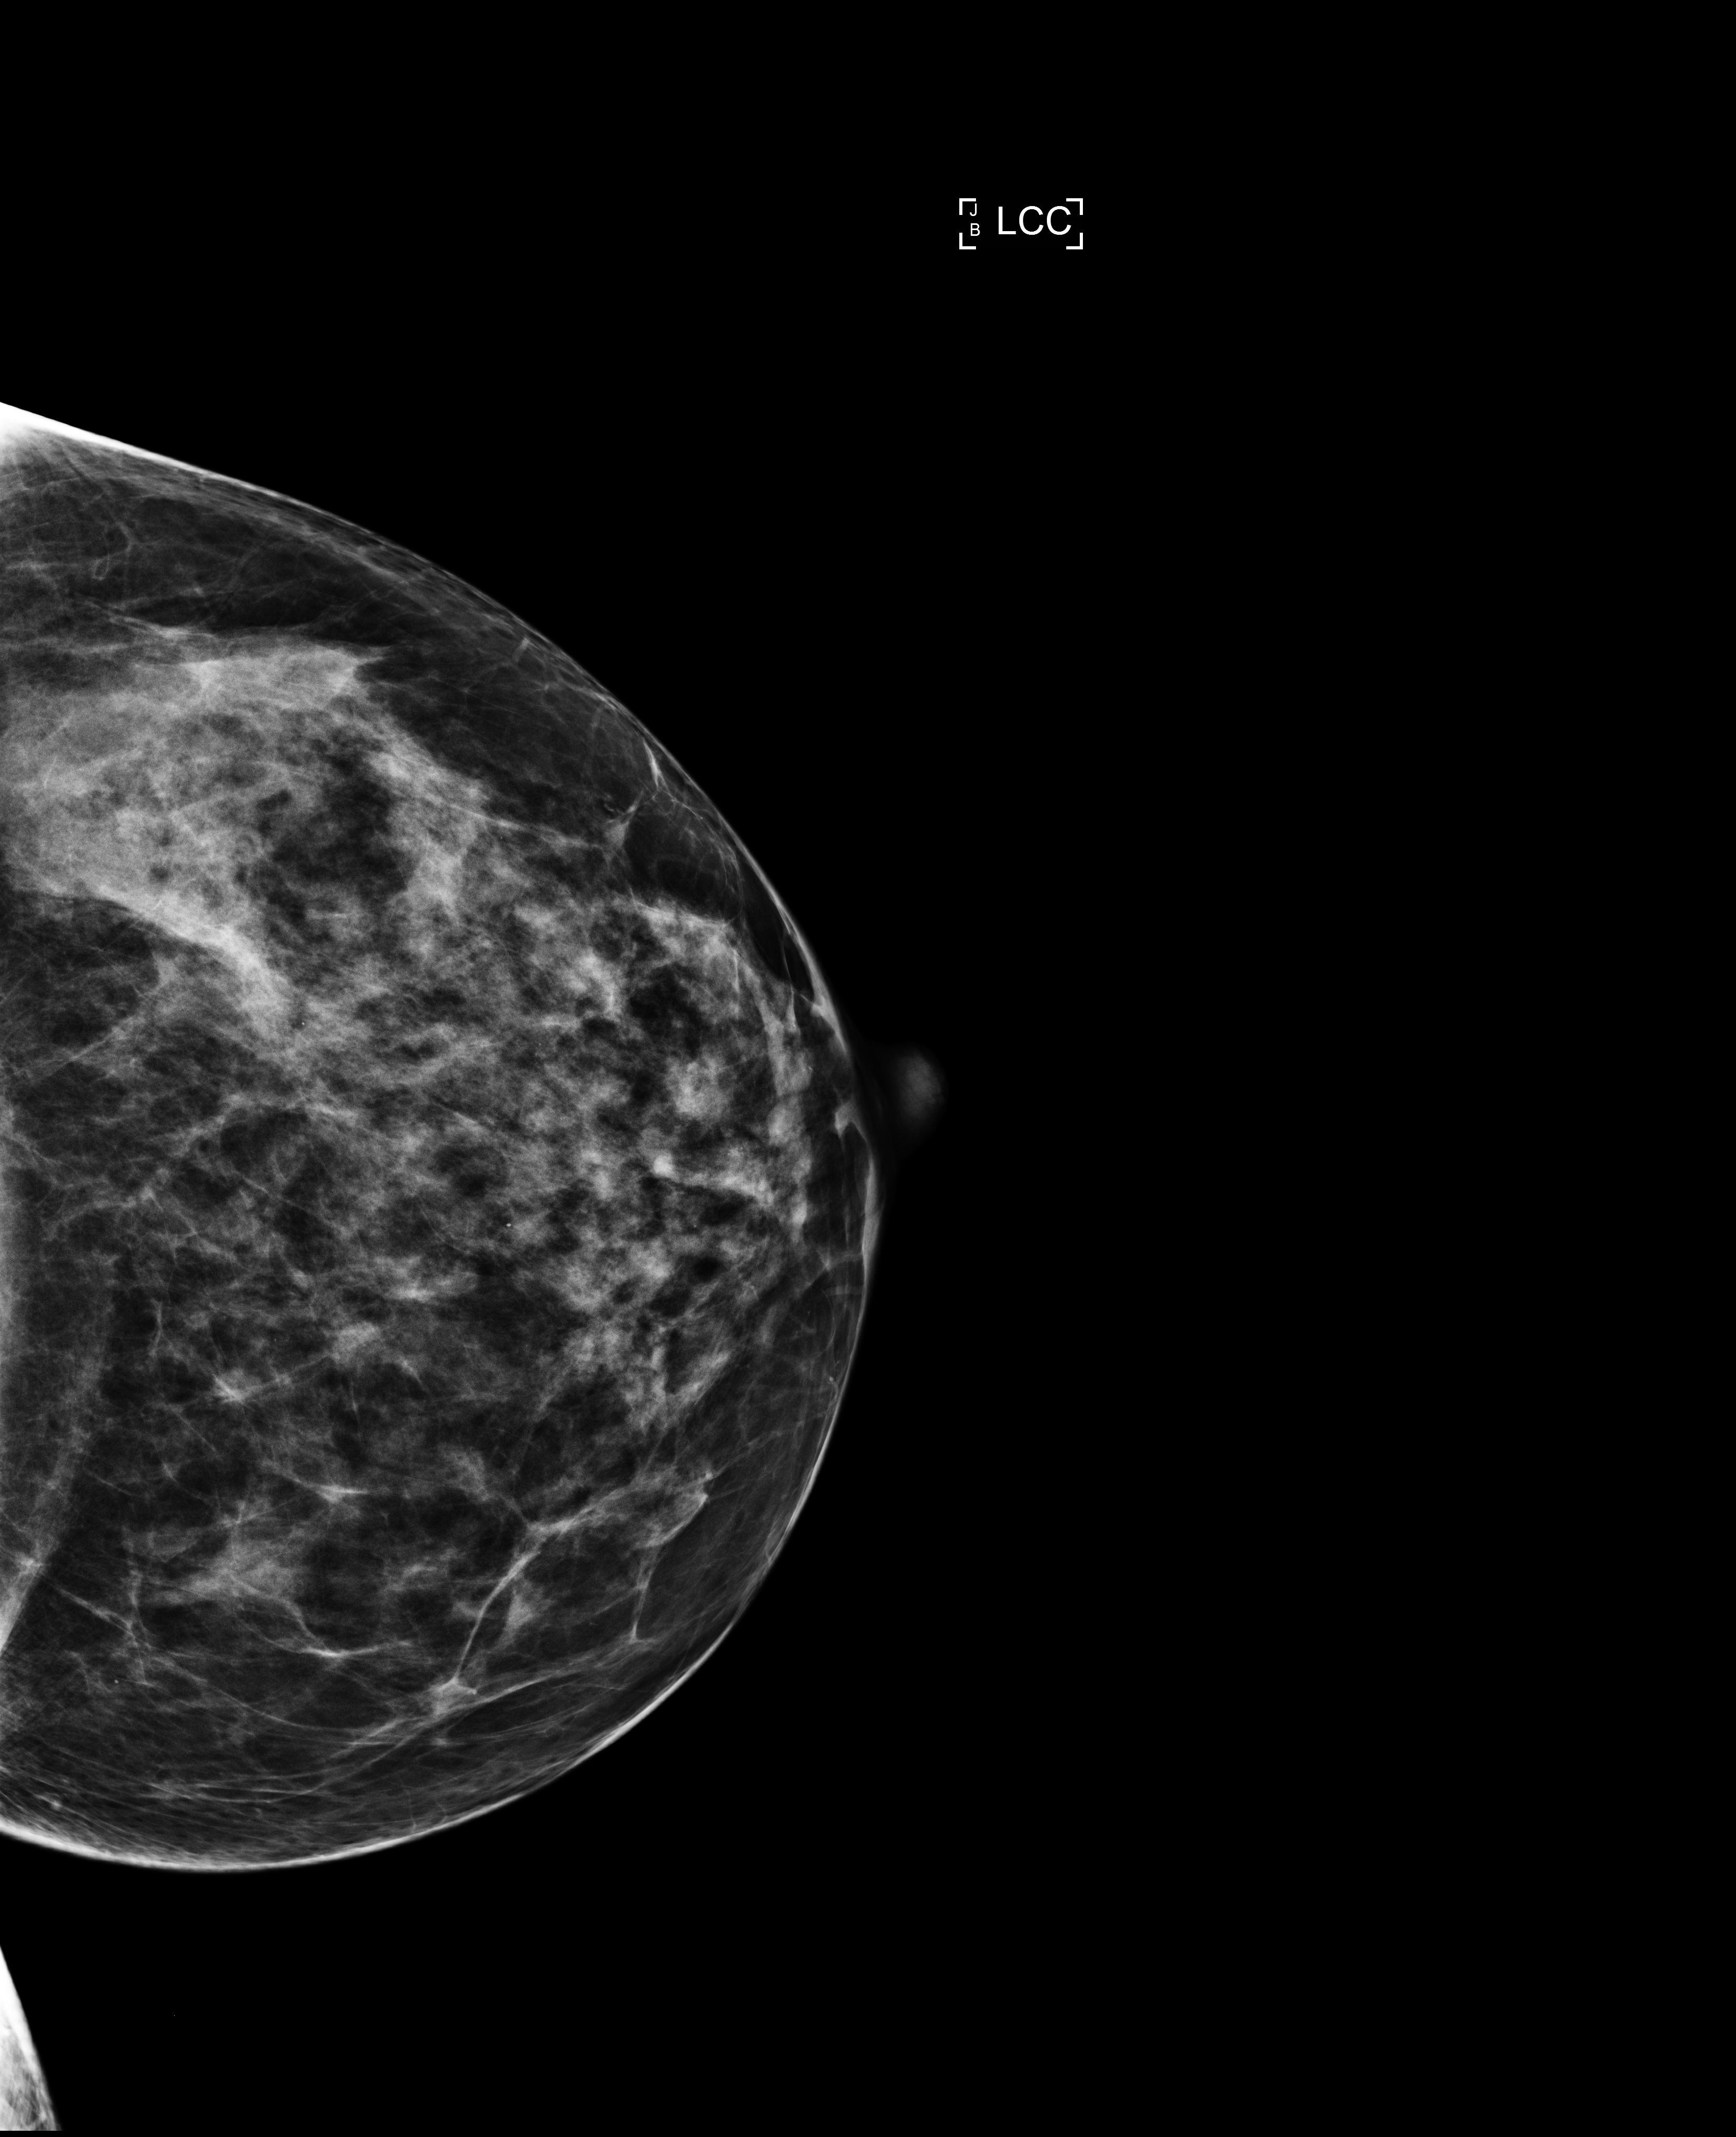
Full-field digital mammogram (FFDM); left breast; cranio-caudal projection; screening examination; compressed breast thickness 81 mm. Female patient, age 47 years.
- breast density at the screening exam (both breasts): heterogeneously dense (BI-RADS density category c)
- final BI-RADS category for the screening round (tomosynthesis exam, both breasts): category 1
- recall: no recall after this screen